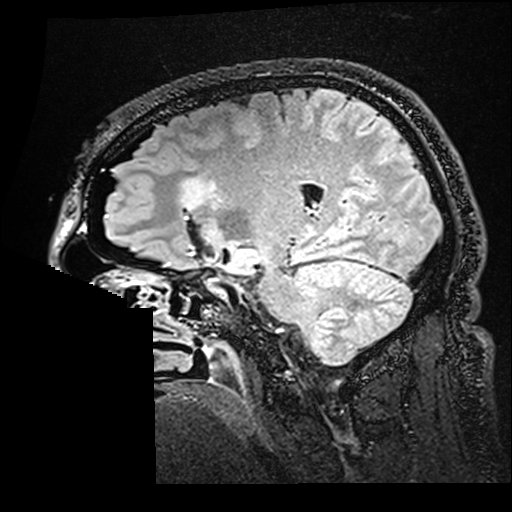
Brain MRI from a brain-tumour surgery series, one sagittal slice. T2 FLAIR. 512 × 512 image matrix, field of view 250 × 250 mm. From the clinical record (not read from this slice): histopathology: Astrocytoma; WHO grade: 2; IDH mutation: yes.
Annotated regions visible in this slice (manually delineated by an expert):
- residual tumour: box from (x=182, y=179) to (x=215, y=209) px